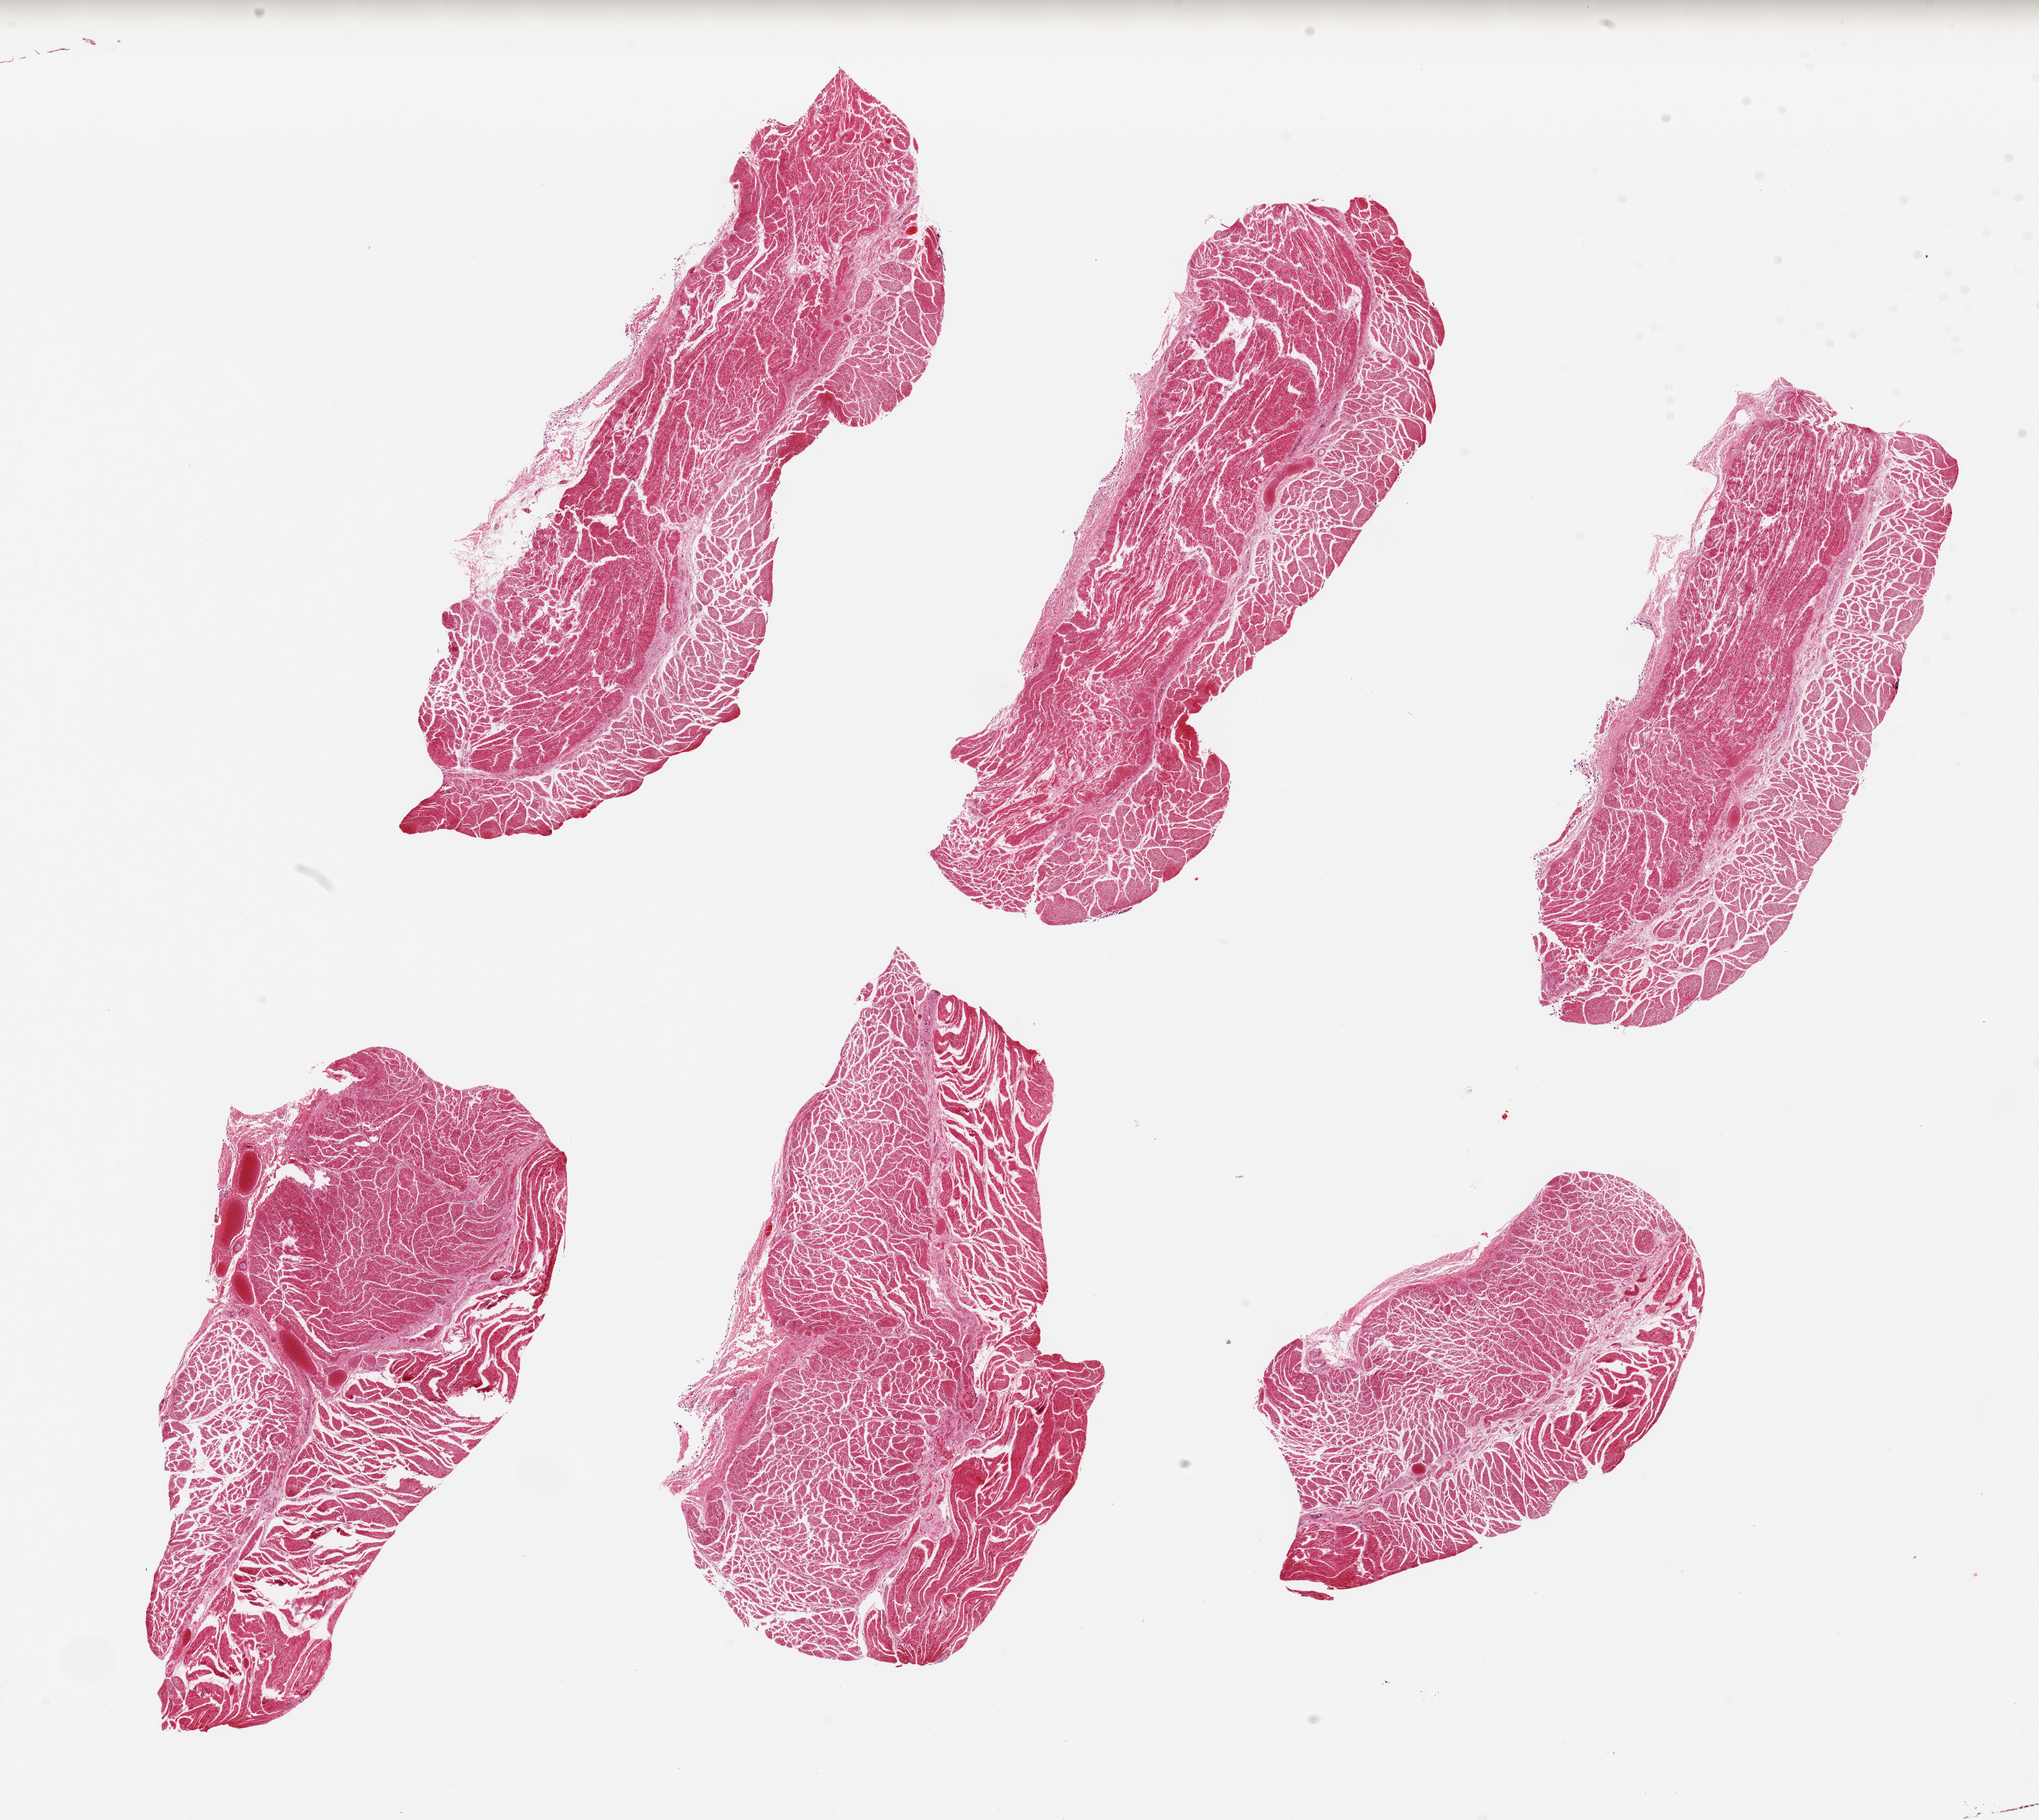
Whole-slide image, hematoxylin and eosin (H&E) stain, brightfield — whole scanned area (about 22.6 x 20.2 mm) shown as a low-resolution overview, PAXgene-fixed, paraffin-embedded tissue, target tissue: esophageal muscle, tissue donor sample. Male donor.
Review note (as recorded): 6 pieces, ~8x3.5mm.